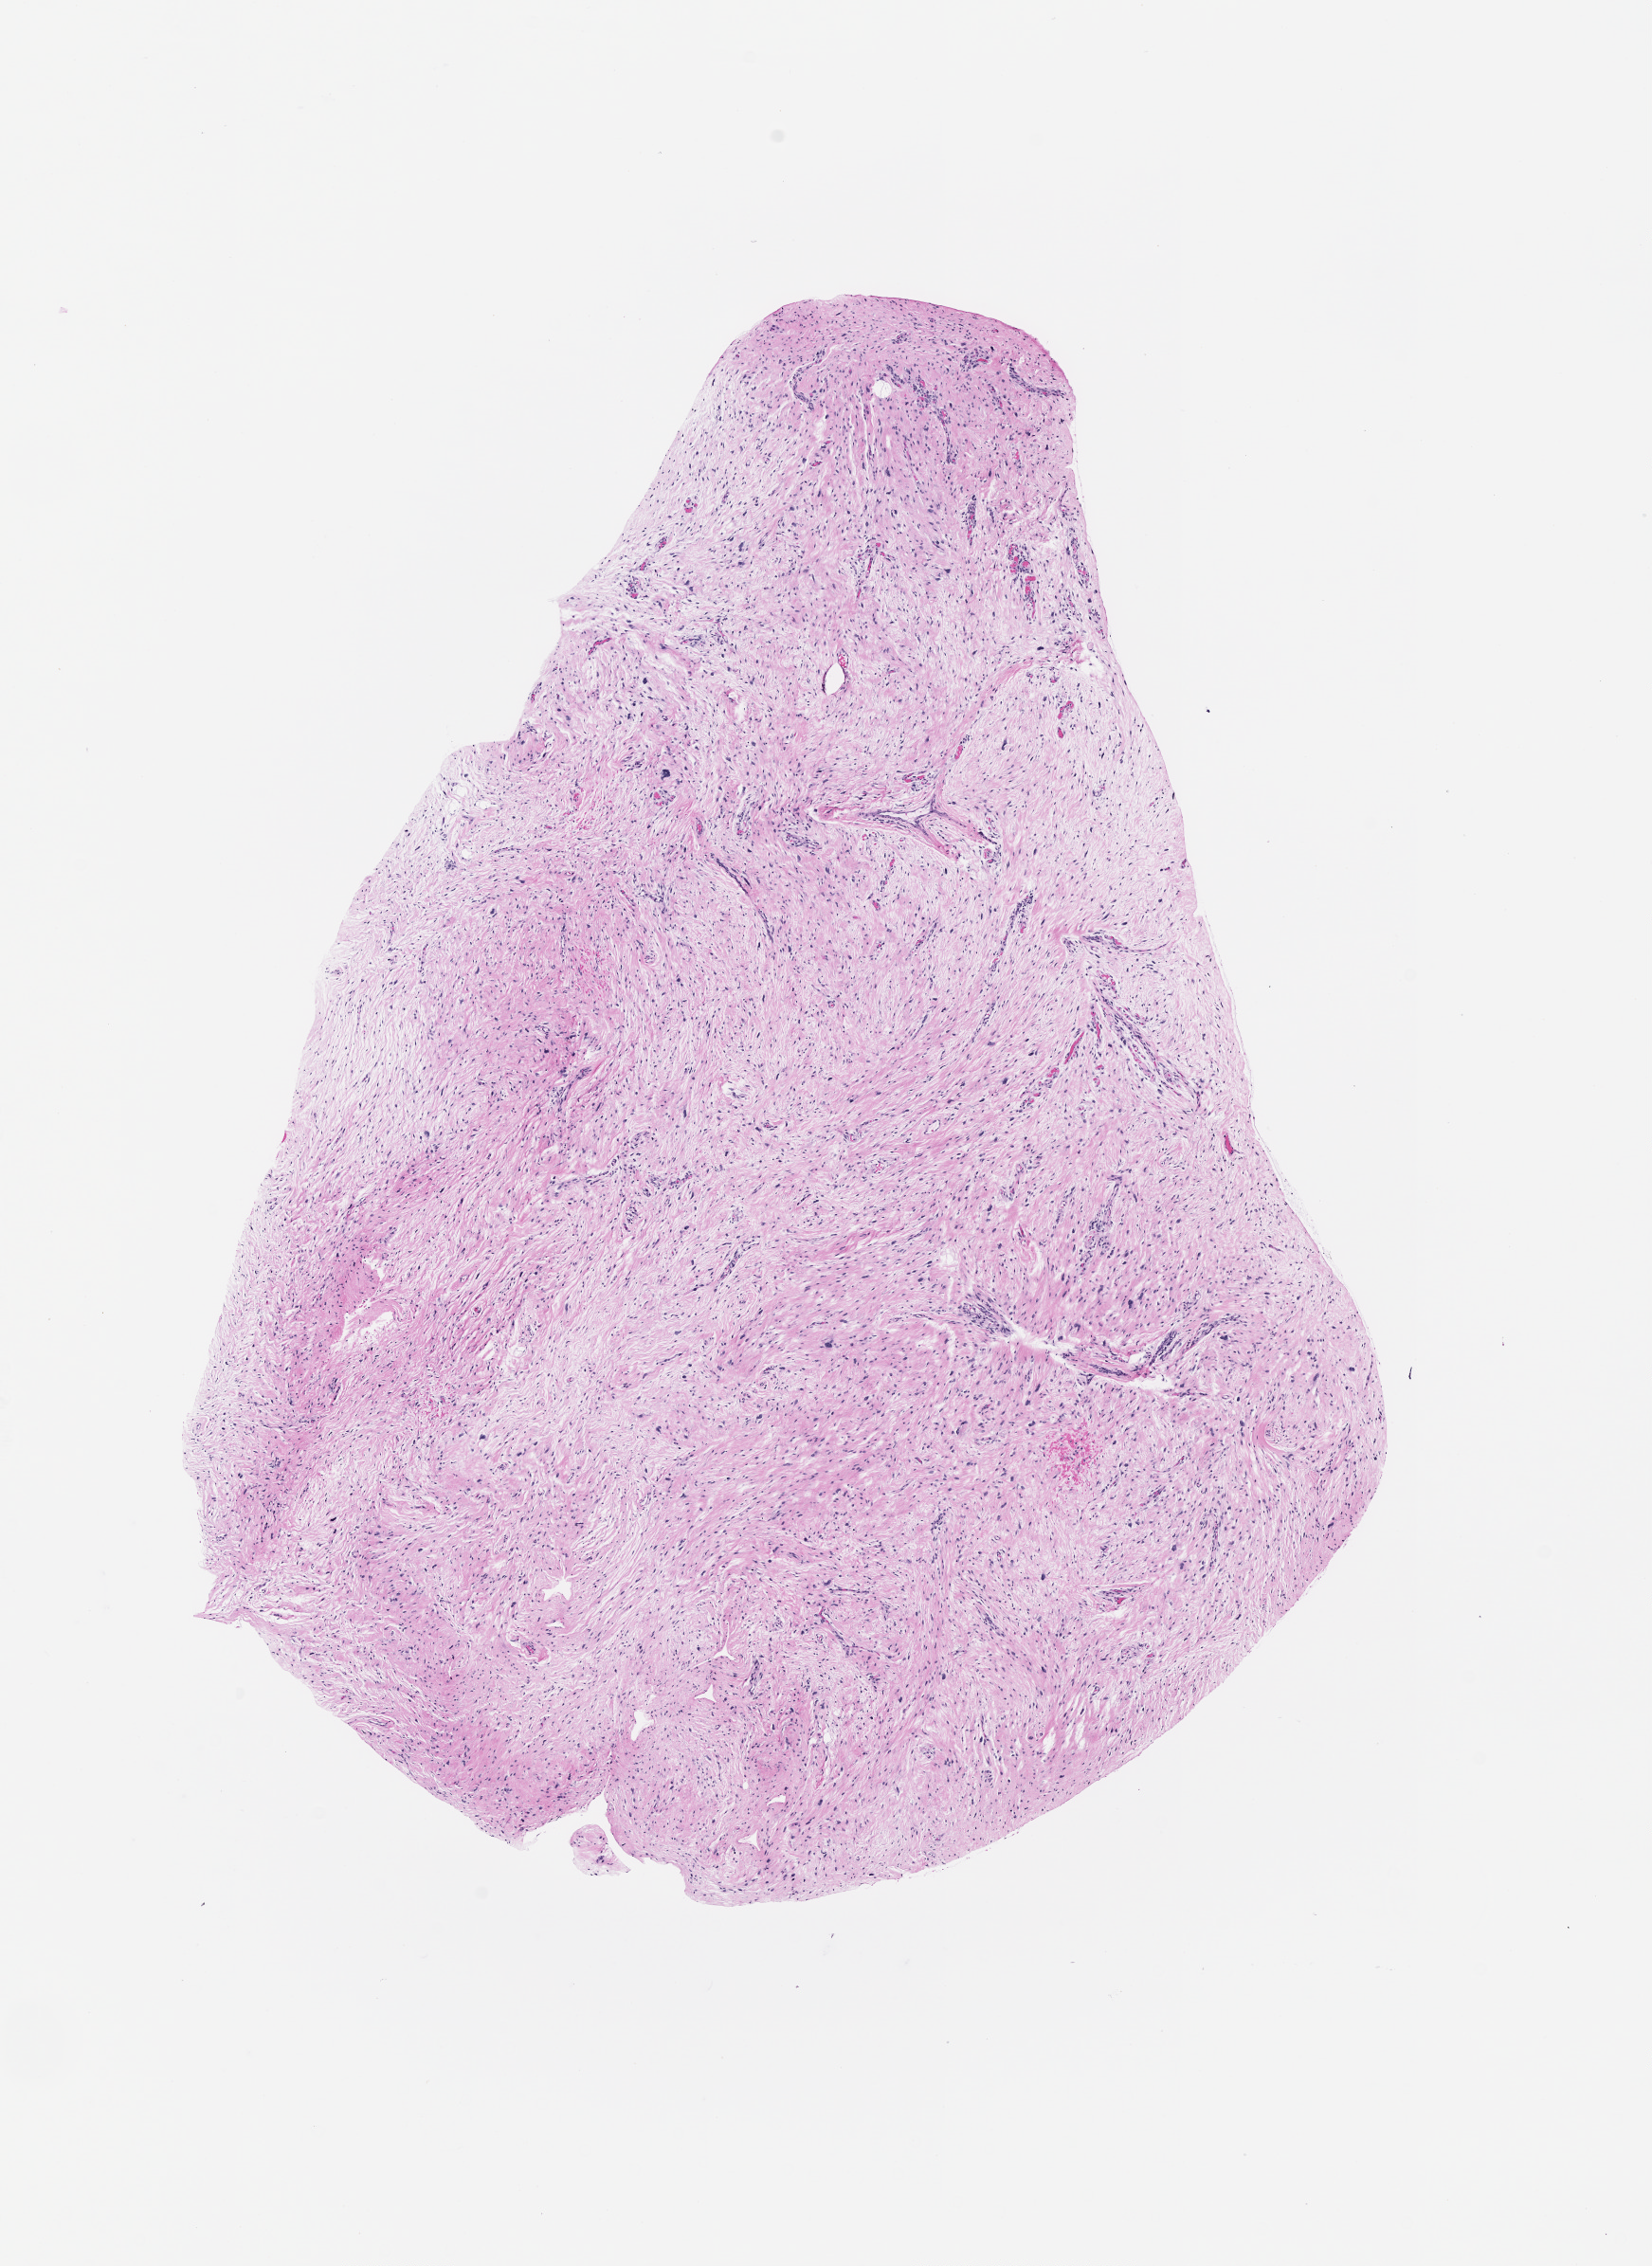
Whole-slide histology image, H&E-stained — whole scanned area (about 7.0 x 9.6 mm, slide scanned at 20x) shown as a low-resolution overview.
Patient diagnosis (cohort enrolment): sarcoma (site not recorded at cohort level).